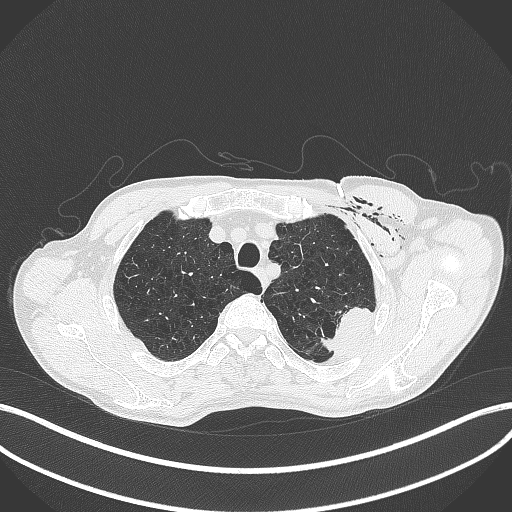
Chest CT, one axial slice. Position 348 of 457 along the scan axis. Lung window (W 1500 / L -600 HU). 1 mm slice thickness. 512 × 512 image matrix, field of view 400 × 400 mm. Male patient, age 58 years. From the clinical record (not read from this slice): clinical TNM (as recorded): T3 N0 M0.
Outlined on this slice (rectangle marked by the reading radiologist):
- lung tumour (recorded histology: adenocarcinoma): bounding box <317,303,373,357> (left, top, right, bottom; pixels)